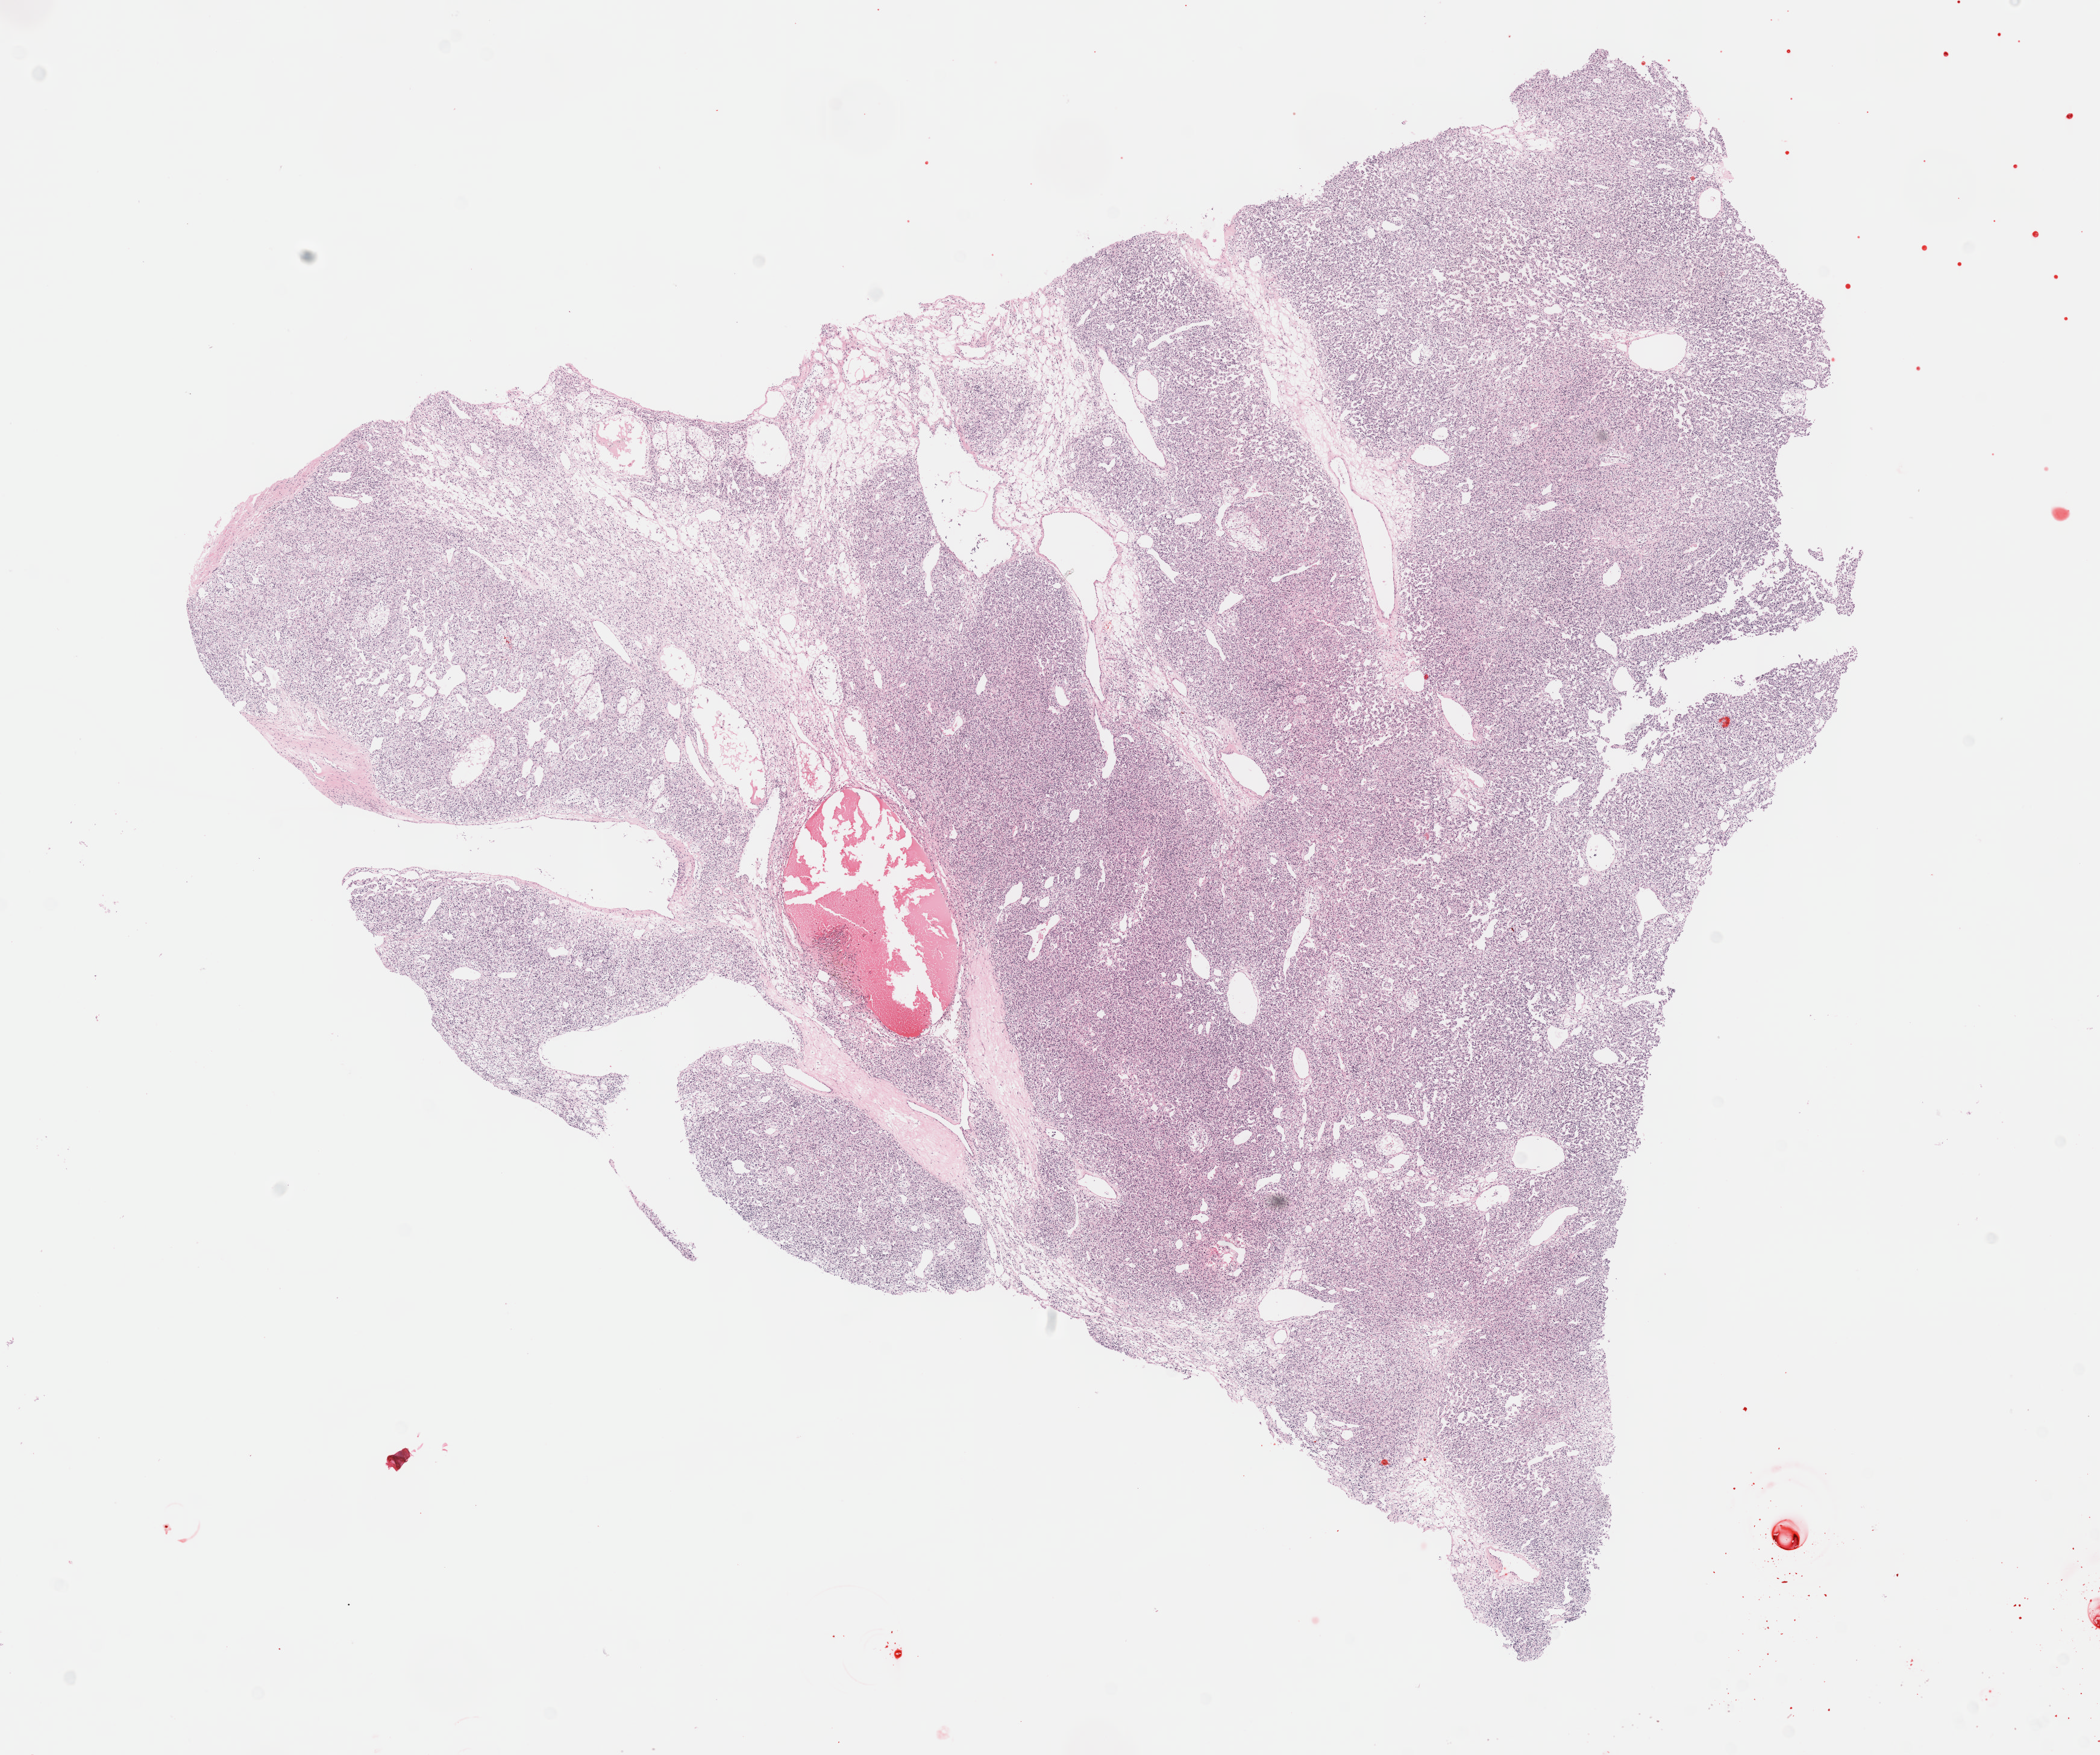
Hematoxylin and eosin (H&E) stained whole-slide image — low-resolution overview of the scanned area, about 14.1 x 11.8 mm, formalin-fixed paraffin-embedded (FFPE) diagnostic section, primary tumour sample from the kidney. Female patient. Histologic grade: G2 (moderately differentiated).
AJCC pathologic stage: I. Diagnosis: Clear cell adenocarcinoma, NOS.